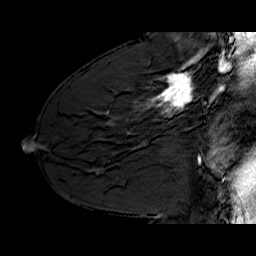
Breast MRI (dynamic contrast-enhanced), one sagittal slice; slice 37 of 60 in the series (ordered by position); dynamic contrast-enhanced series, time point 2 of 6 at this slice position (early post-contrast); 1.5 T; TE 6.4 ms, TR 32.9 ms; 4 mm slice thickness; 256 × 256 image matrix, field of view 200 × 200 mm. Female patient. Case-level facts recorded for this patient, not image findings: setting: breast cancer imaged before/during neoadjuvant chemotherapy; receptor status: HER2-positive.
Outlined on this slice (semi-automatically segmented with operator editing):
- analysis volume of interest (the breast-tissue region the enhancement analysis was run in; not a lesion): box from (x=130, y=62) to (x=210, y=128) px
- tumour enhancement mask (voxels above the 100 % enhancement threshold inside the analysis volume of interest): (x=152, y=62)–(x=192, y=116)